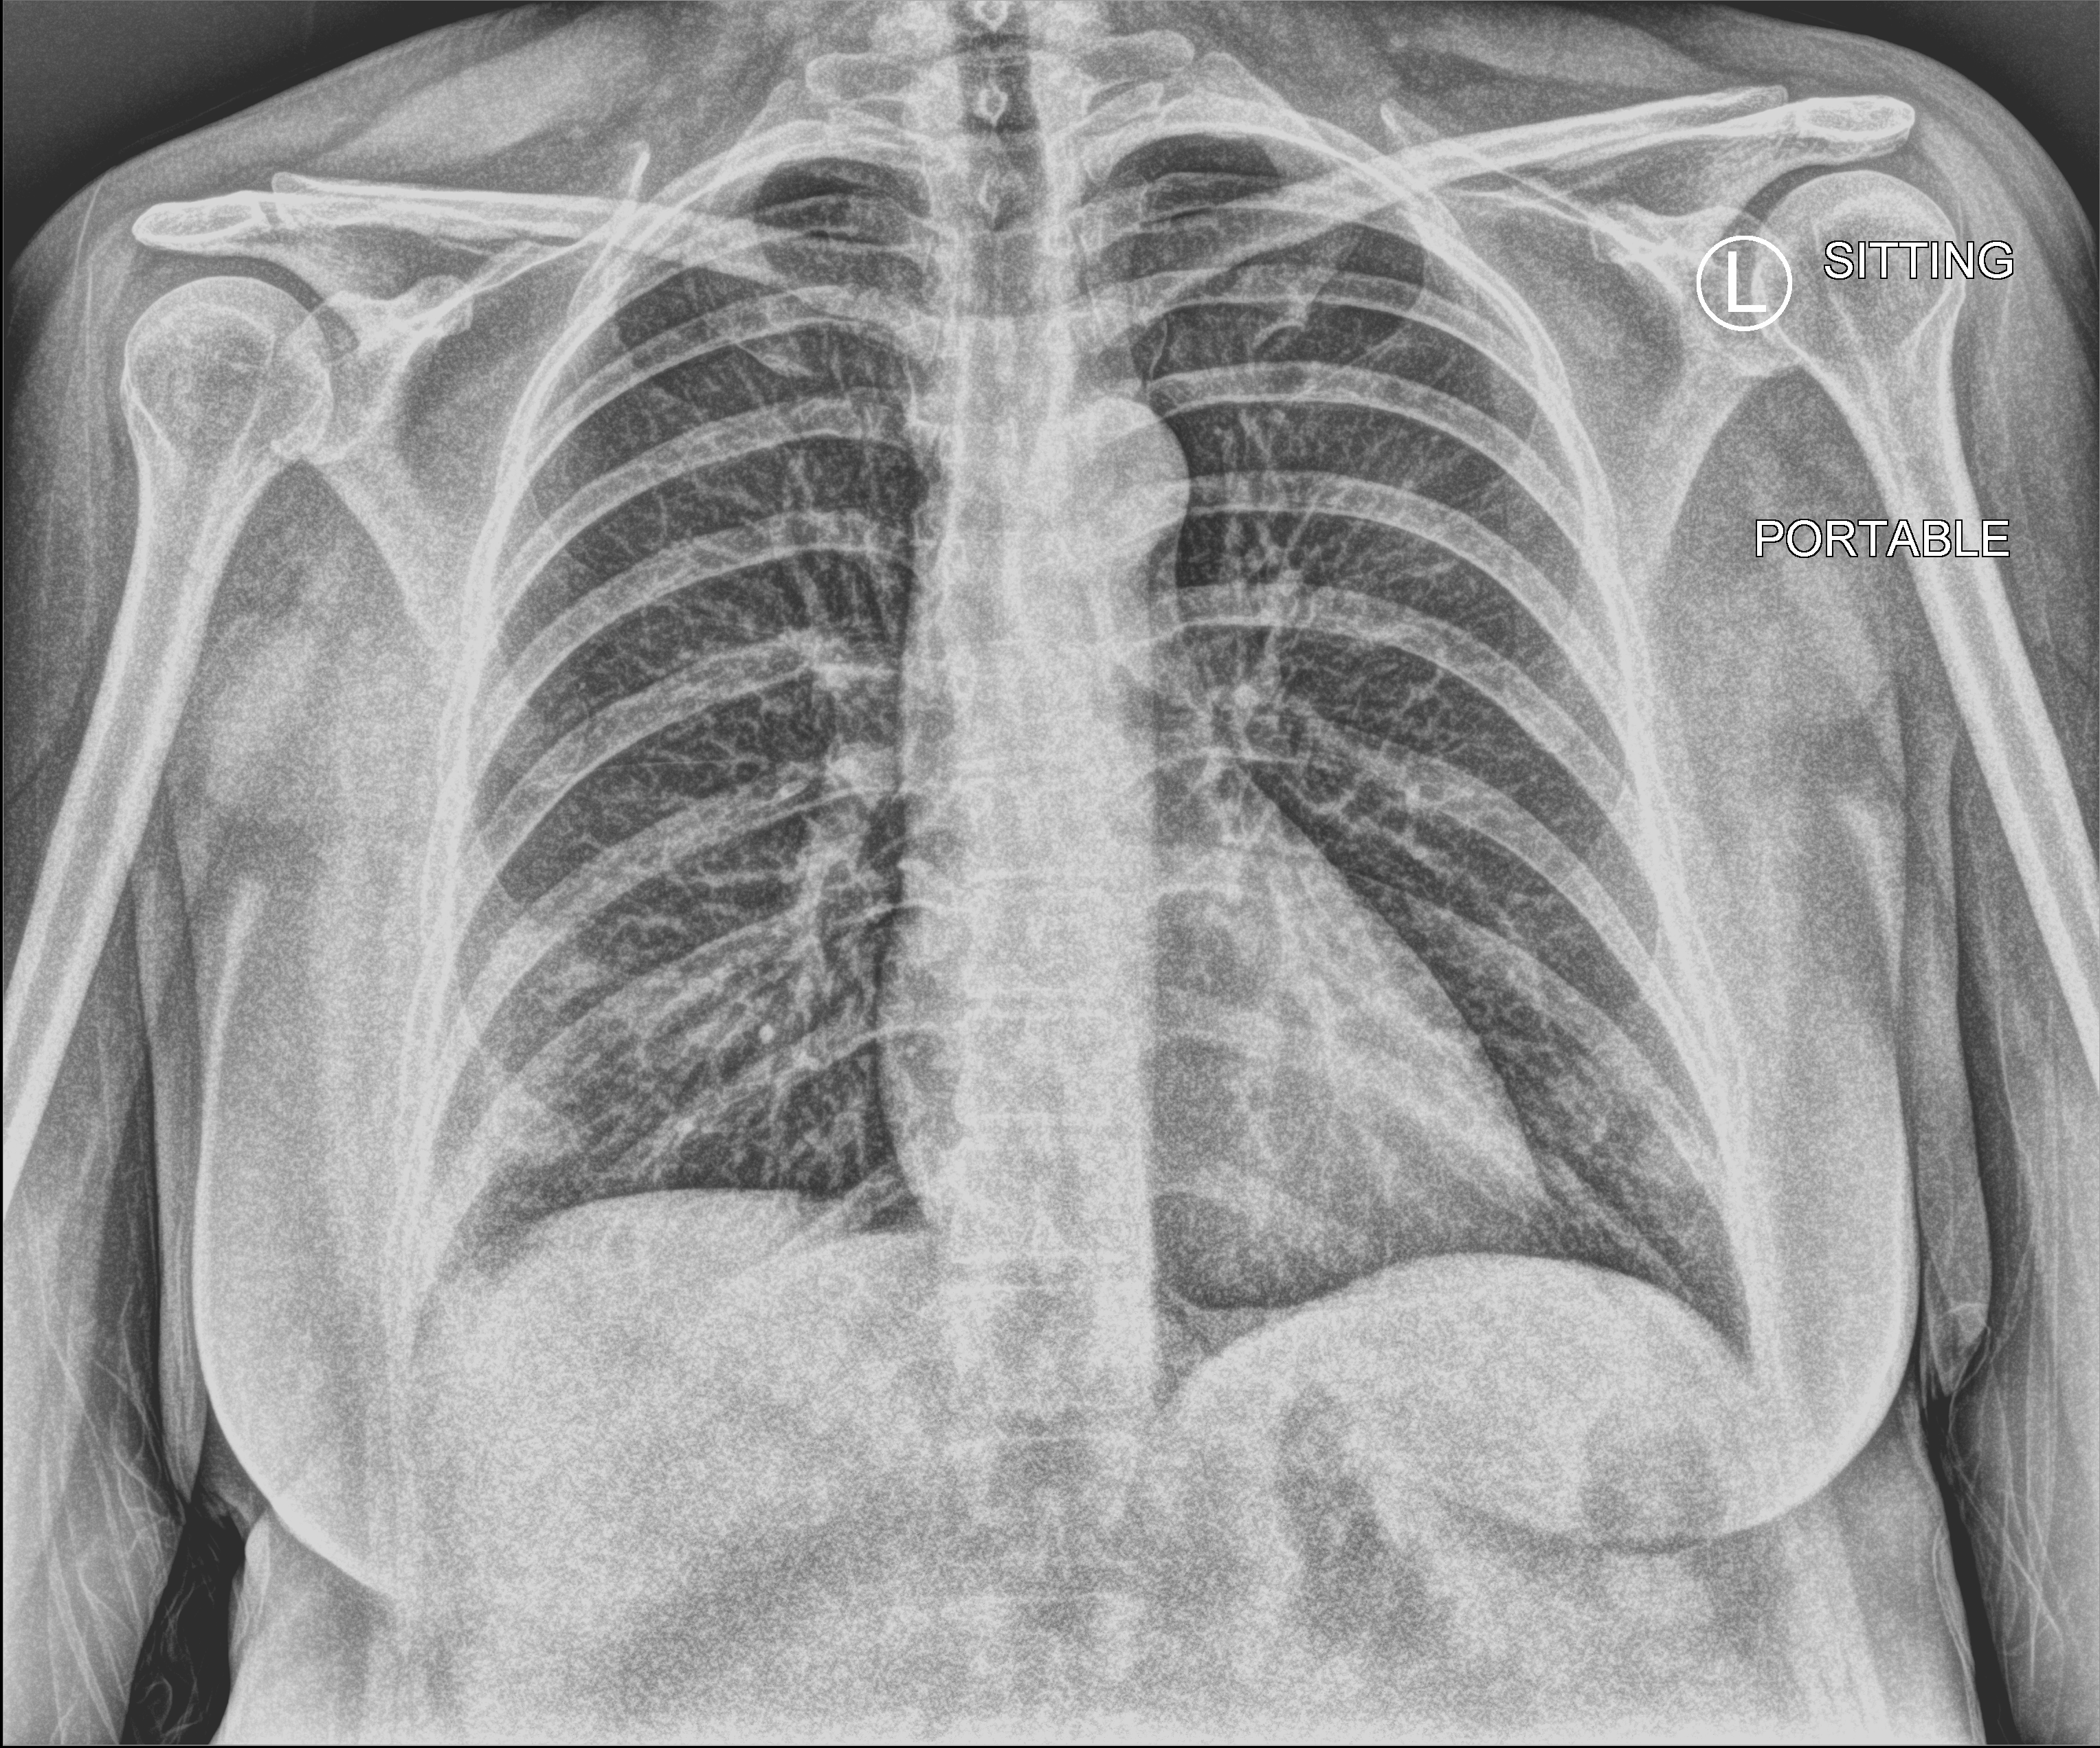
Chest X-ray (portable); anteroposterior (AP) projection. Female patient hospitalised with COVID-19, age 18–59 years.
From the hospital-stay record, not from the radiograph (when in the stay this image was taken is not recorded): mechanically ventilated during this hospital stay: no; admitted to intensive care during this hospital stay: no; hypertension (admission record): no.